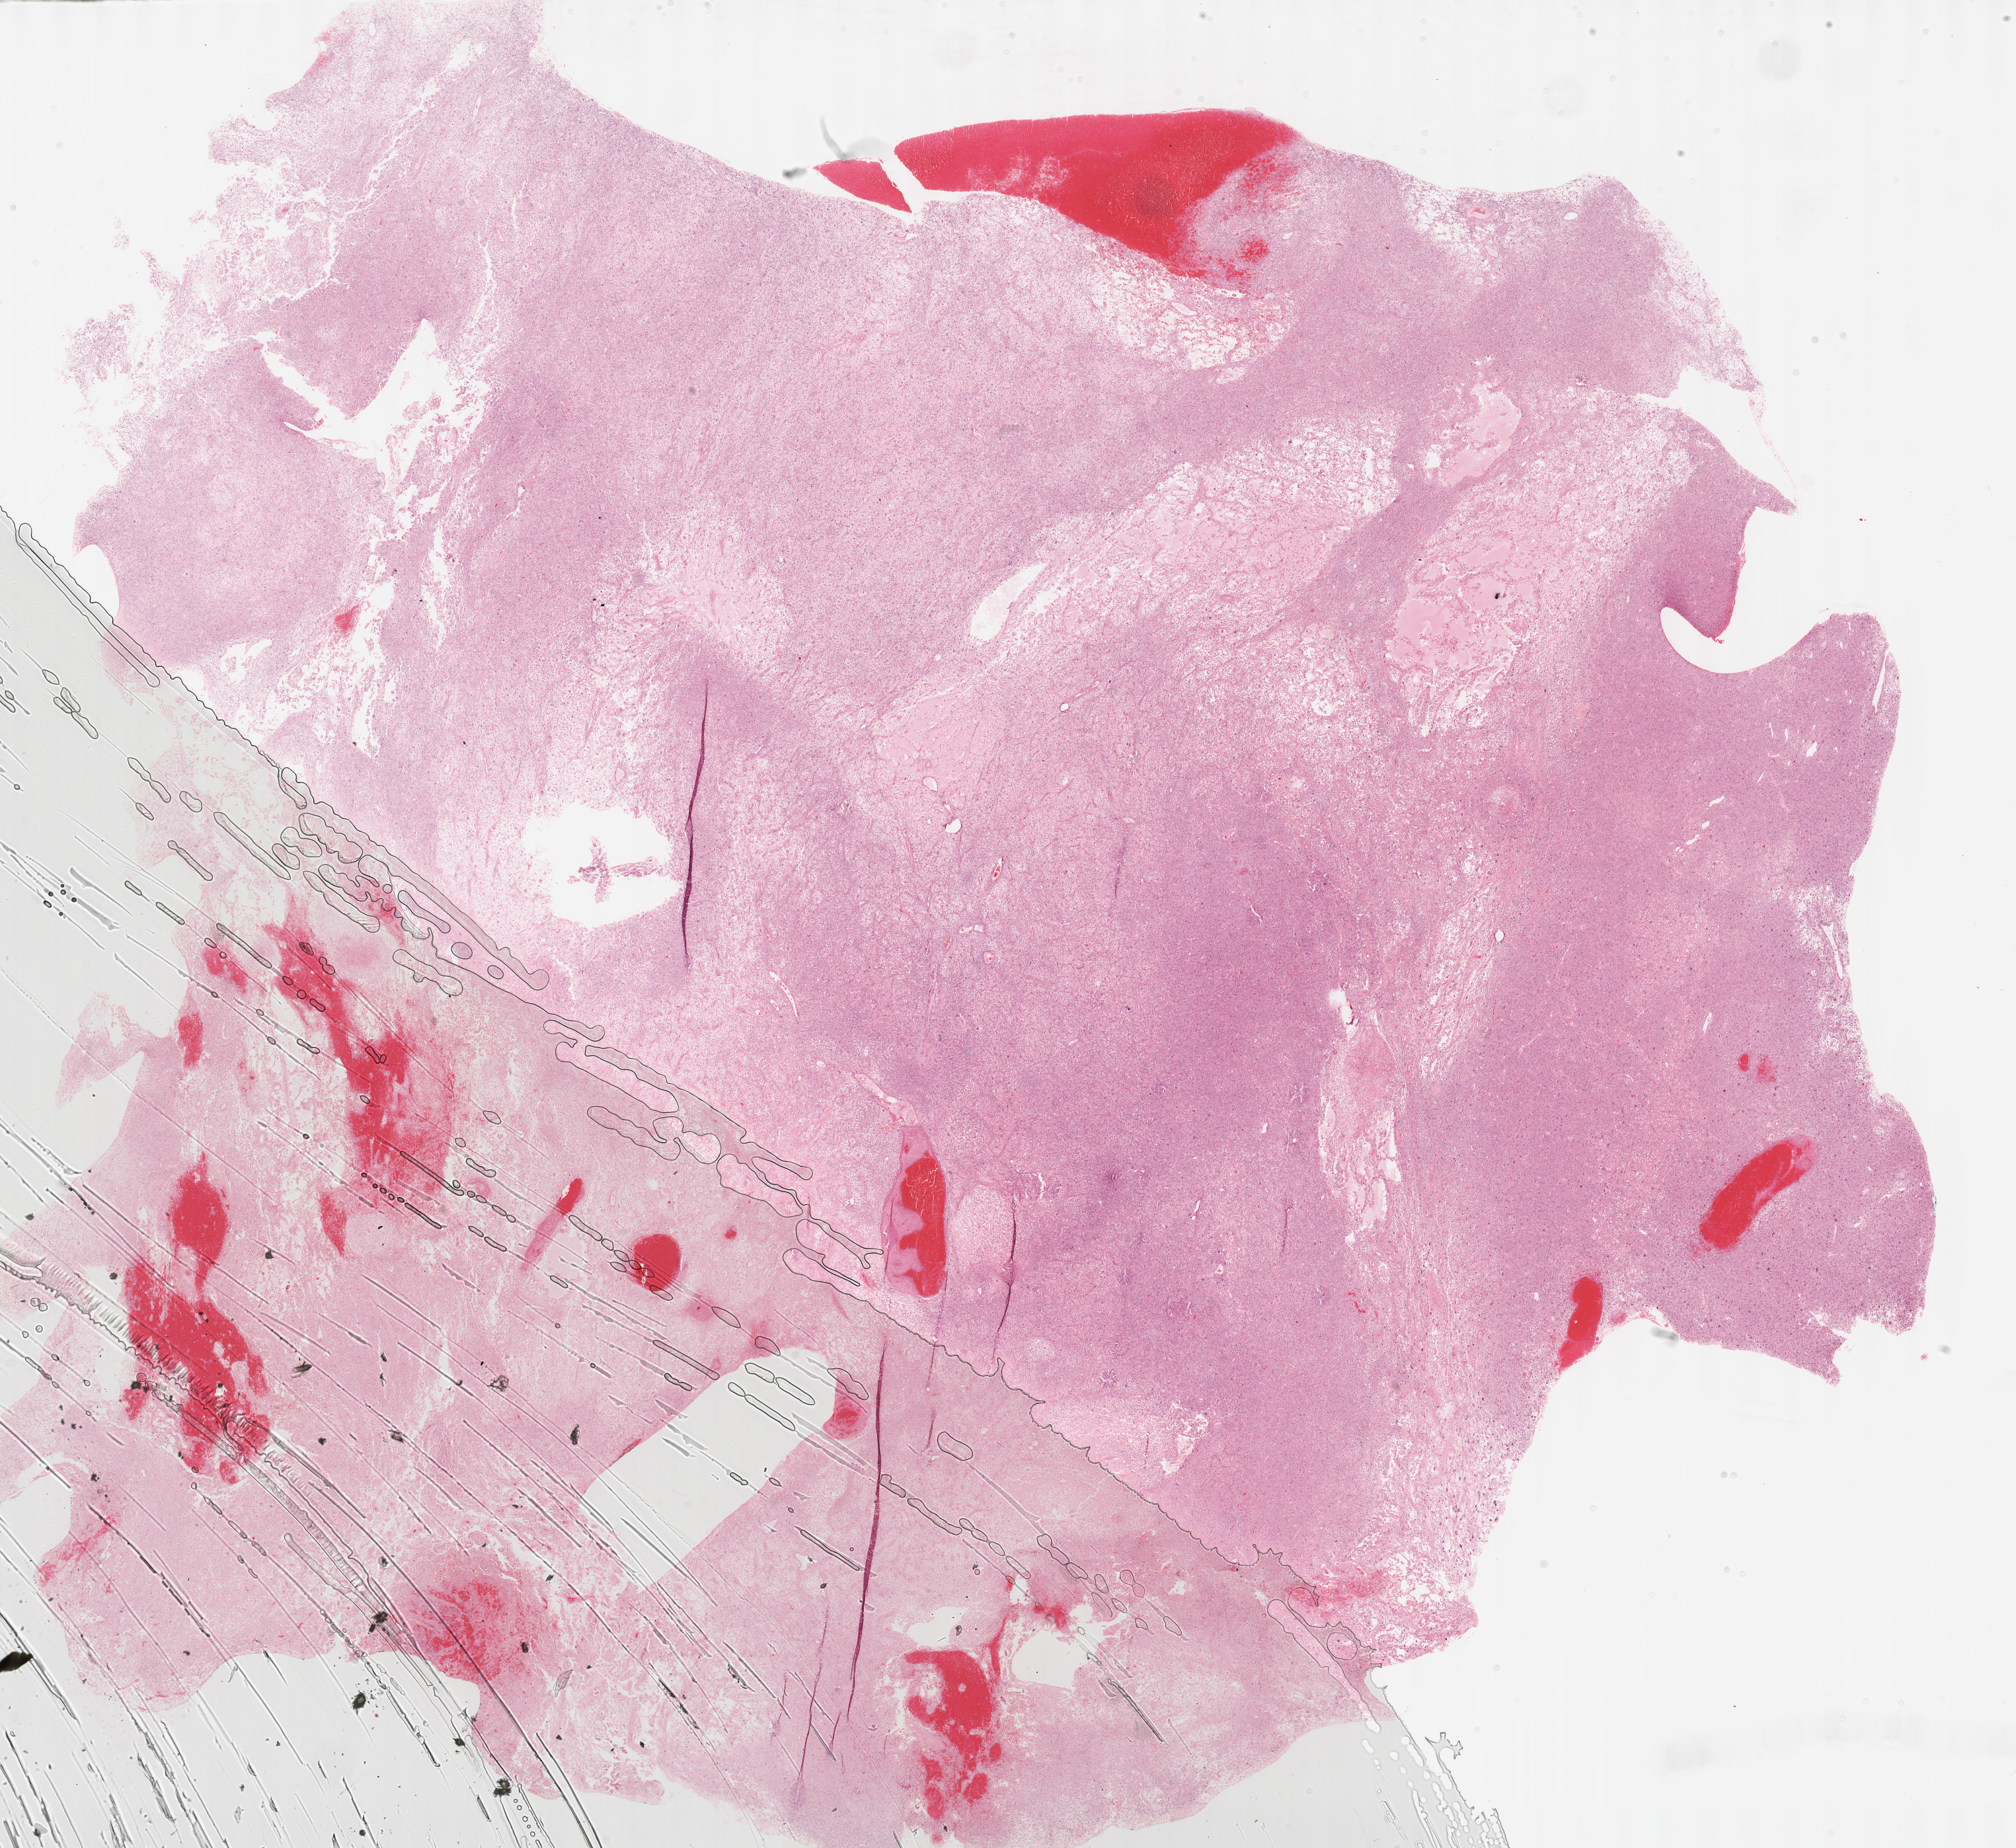
Whole-slide histology image, H&E-stained — whole scanned area (about 24.6 x 22.6 mm) shown as a low-resolution overview, FFPE section, primary tumour sample from the connective, subcutaneous and other soft tissues. Female, age 63 years at initial diagnosis.
Histologic diagnosis: Malignant fibrous histiocytoma (connective, subcutaneous and other soft tissues of lower limb and hip).